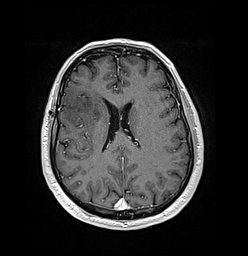
Brain MRI from a brain-tumour surgery series, one axial slice; slice 65 of 176 in the series (ordered by position); T1-weighted post-contrast; 248 × 256 image matrix, field of view 242 × 250 mm. Case-level facts recorded for this patient, not image findings: histopathology: Oligodendroglioma; WHO grade: 3; IDH mutation: yes; tumour location: Right Frontal.
Outlined on this slice (outlined manually by an expert reader):
- tumour: box from (x=75, y=117) to (x=81, y=124) px